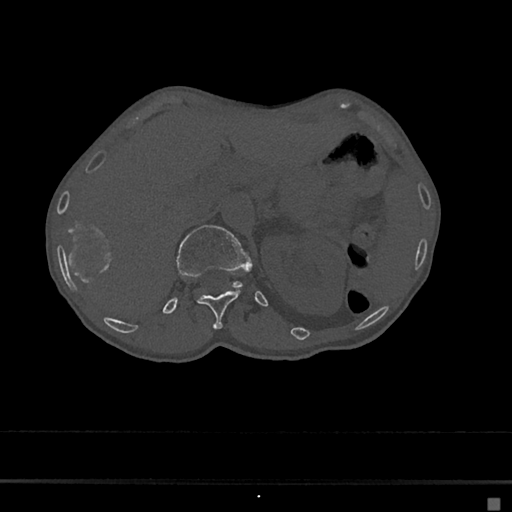
CT including the spine, one axial slice. Position 104 of 797 along the scan axis. Bone window (W 1800 / L 400 HU). 512 × 512 image matrix, field of view 360 × 360 mm. Patient: female, 68 years. Case-level facts recorded for this patient, not image findings: primary cancer: renal.
Outlined on this slice (semi-automatically segmented with operator editing):
- L1 vertebra: bounding box [x1, y1, x2, y2] px = [175, 225, 252, 287]
- T12 vertebra: [197, 291, 238, 329]